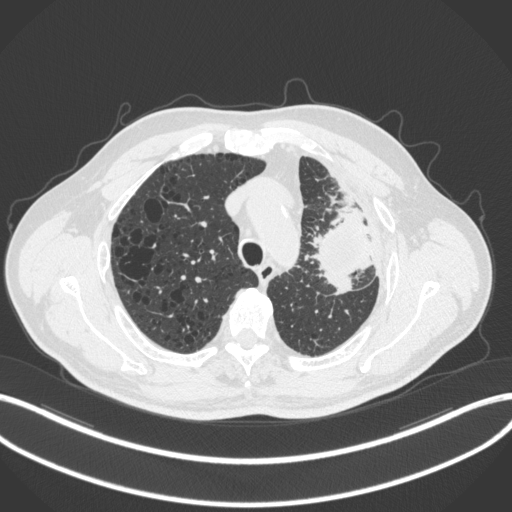
Chest CT, one axial slice. Slice 234 of 286 in the series (ordered by position). Reconstruction kernel B31f. 120 kVp. Lung window (W 1500 / L -600 HU). 1 mm slice thickness. 512 × 512 image matrix, field of view 400 × 400 mm. Male patient, age 68 years. Case-level facts recorded for this patient, not image findings: clinical TNM (as recorded): T3 N3 M1.
Annotated regions visible in this slice (bounding box drawn by a radiologist):
- lung tumour (recorded histology: adenocarcinoma): box from (x=313, y=201) to (x=374, y=300) px